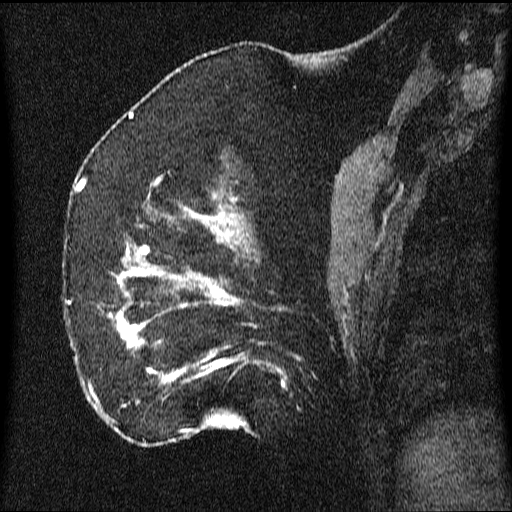
Breast MRI (dynamic contrast-enhanced), one sagittal slice; slice 20 of 64 in the series (ordered by position); dynamic contrast-enhanced series, image 2 of 3 at this slice position (ordered by acquisition); 1.5 T; TE 4.2 ms, TR 9.1 ms; 512 × 512 image matrix, field of view 180 × 180 mm. Patient: female, 52 years.
Annotated regions visible in this slice (semi-automatically segmented with operator editing):
- analysis volume of interest (the breast-tissue region the enhancement analysis was run in; not a lesion): box from (x=64, y=203) to (x=350, y=438) px
- tumour enhancement mask (voxels above the 70 % enhancement threshold inside the analysis volume of interest): (x=111, y=206)–(x=286, y=388)